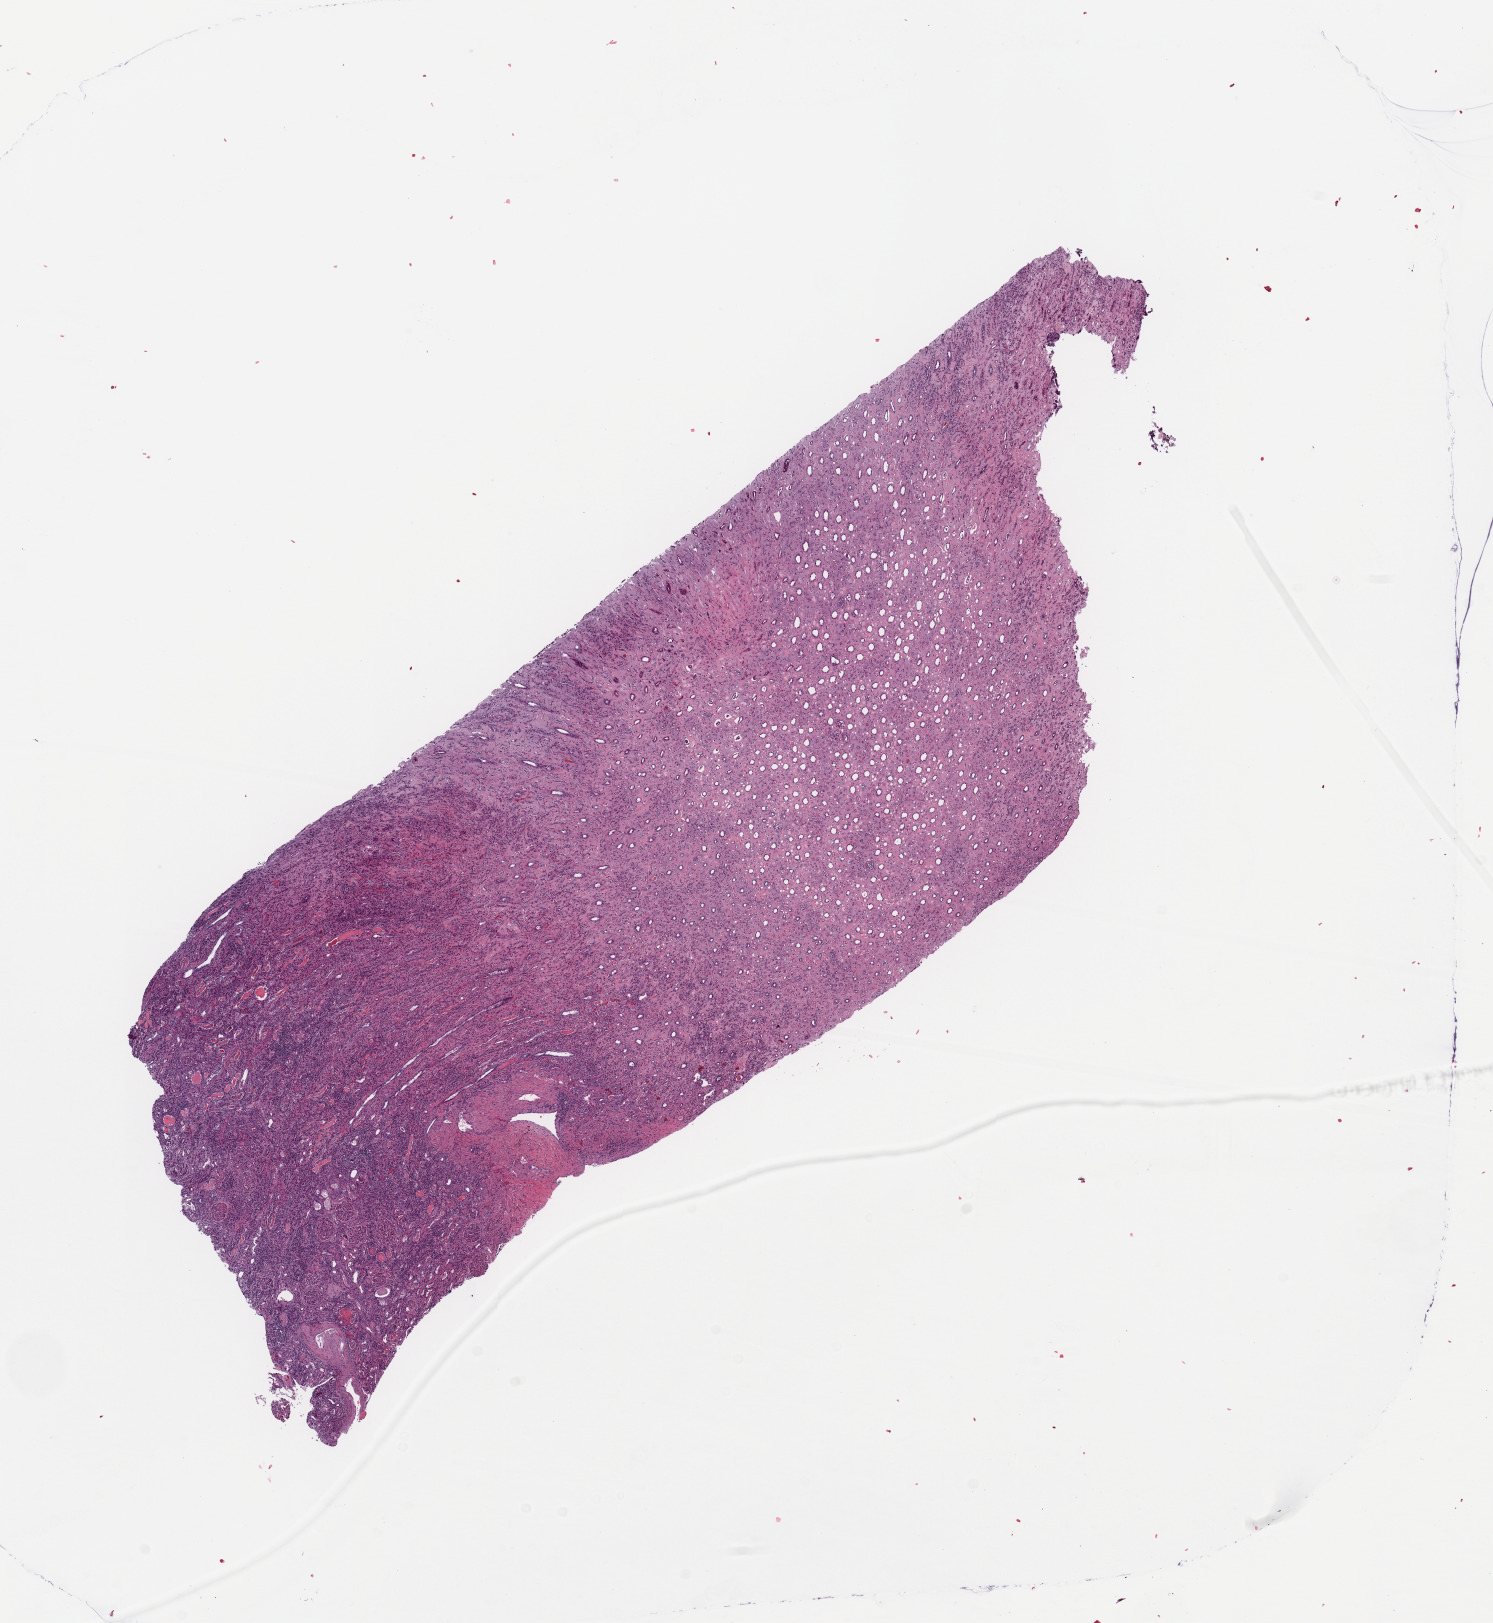
H&E whole-slide image — low-resolution overview of the scanned area, about 11.8 x 12.8 mm (acquisition: 20x scan). Normal (non-tumour) tissue sample, kidney. Patient: male, age 47 years.
This section: normal (non-tumour) tissue from the same patient. Patient diagnosis: Renal cell carcinoma, NOS.